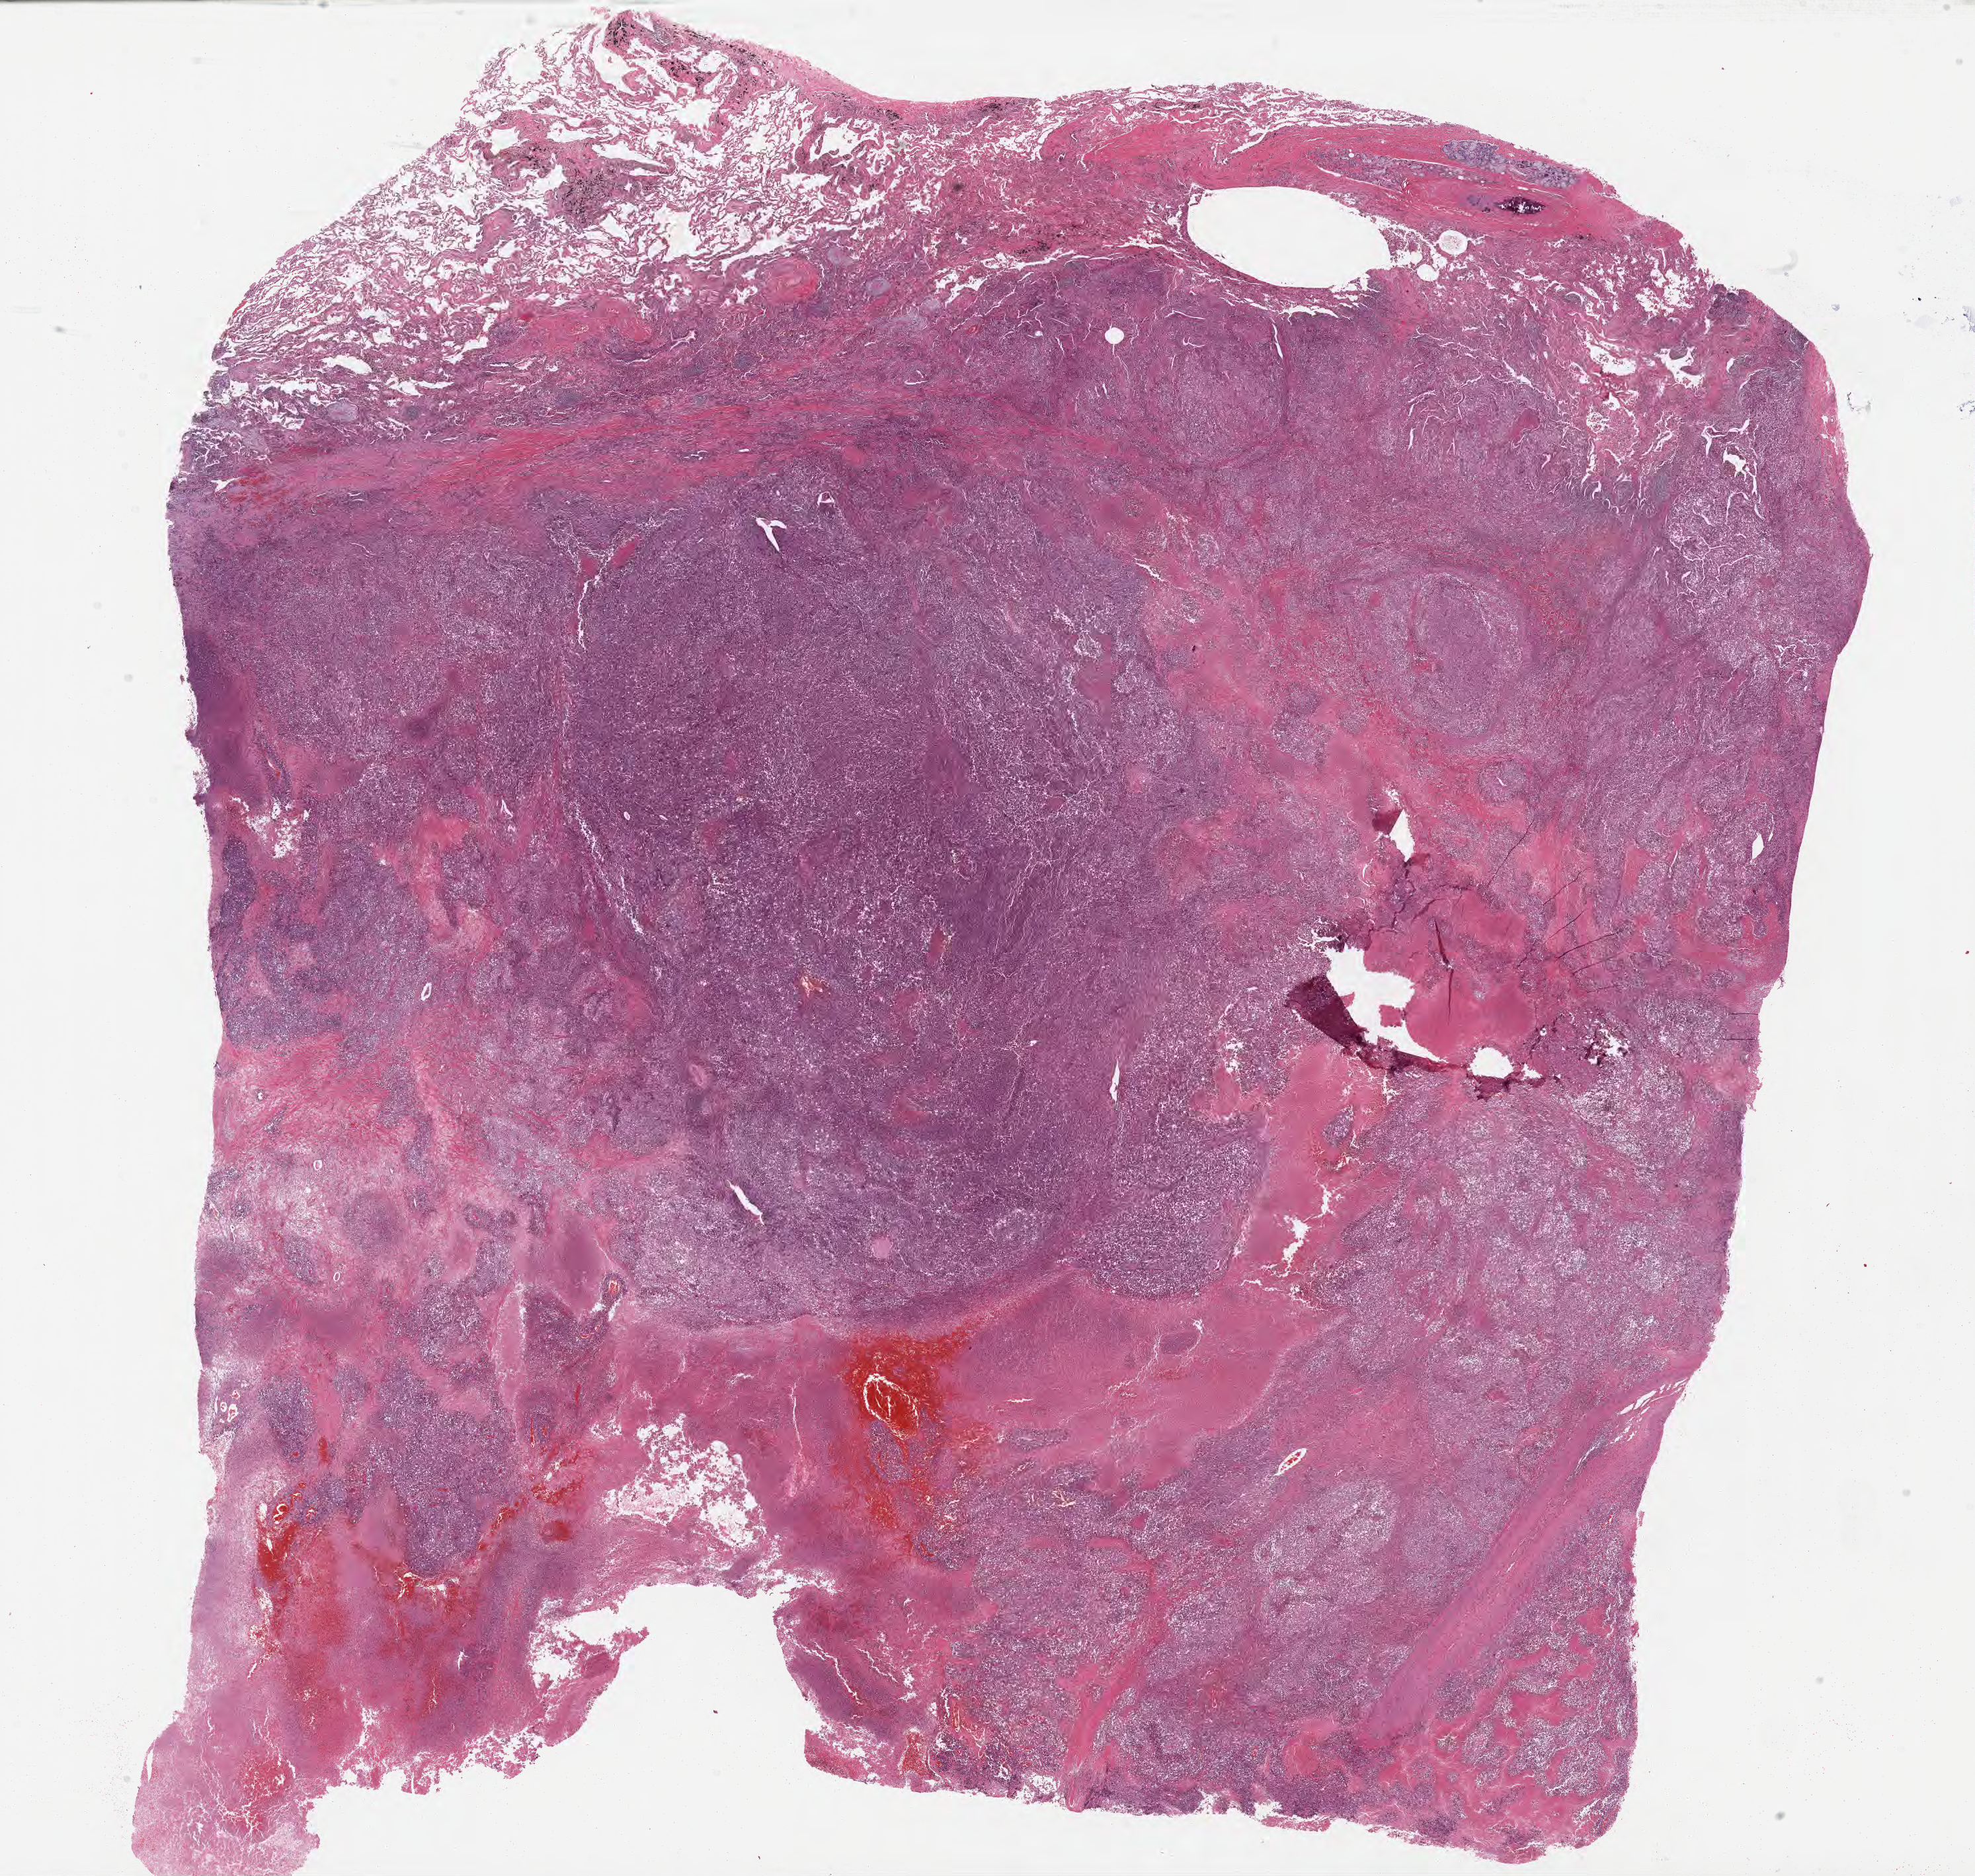
Whole-slide image, hematoxylin and eosin (H&E) stain — low-resolution overview of the scanned area, about 24.2 x 22.9 mm; FFPE section; specimen: primary tumor; anatomic site: upper lobe of left lung. Patient male; 59 years old.
Histologic diagnosis: Adenocarcinoma, NOS.